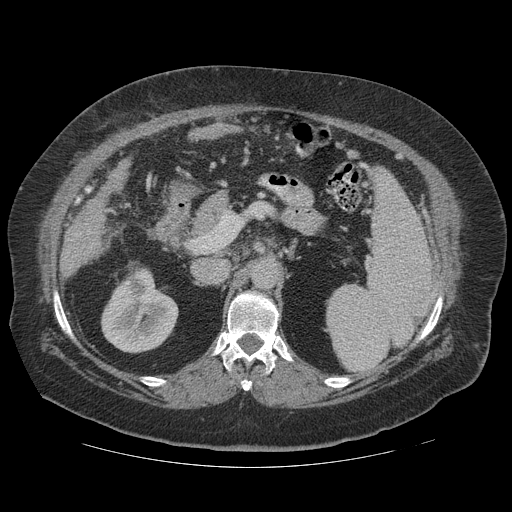
Contrast-enhanced abdominal CT (liver protocol), one axial slice; reconstruction kernel STANDARD; soft-tissue window (W 400 / L 40 HU); 2.5 mm slice thickness; 512 × 512 image matrix, field of view 420 × 420 mm. Case-level facts recorded for this patient, not image findings: diagnosis: hepatocellular carcinoma (patient treated with transarterial chemoembolisation; whether this scan precedes or follows treatment is not stated here); TNM stage (as recorded): Stage-IIIA; Child-Pugh class: A; tumour differentiation: well differentiated; tumour nodularity: multinodular.
Annotated regions visible in this slice (semi-automatic segmentation, software-assisted and operator-edited):
- liver parenchyma outside the tumour (the mass and vessels are separate outlines, so this box may not span the whole liver): bounding box (x1, y1, x2, y2) in pixels: (60, 198, 102, 276)